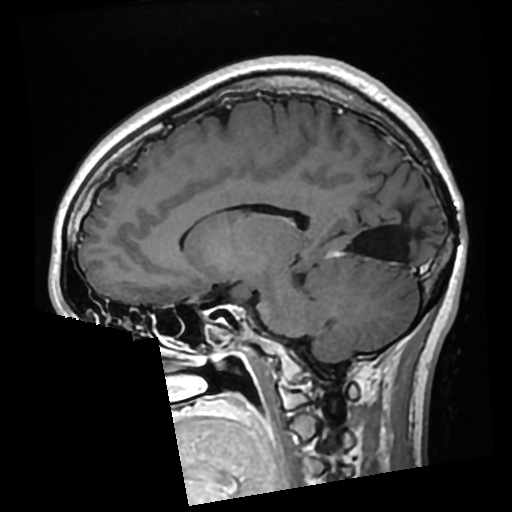
Brain MRI from a brain-tumour surgery series, one sagittal slice. Slice 122 of 276 in the series (ordered by position). T1-weighted post-contrast. 0.7 mm slice thickness. 512 × 512 image matrix, field of view 250 × 250 mm. Case-level facts recorded for this patient, not image findings: histopathology: Glioma with ependymal features; WHO grade: 2; tumour location: Left Parietal.
Outlined on this slice (outlined manually by an expert reader):
- previous resection cavity: bounding box <351,210,406,260> (left, top, right, bottom; pixels)